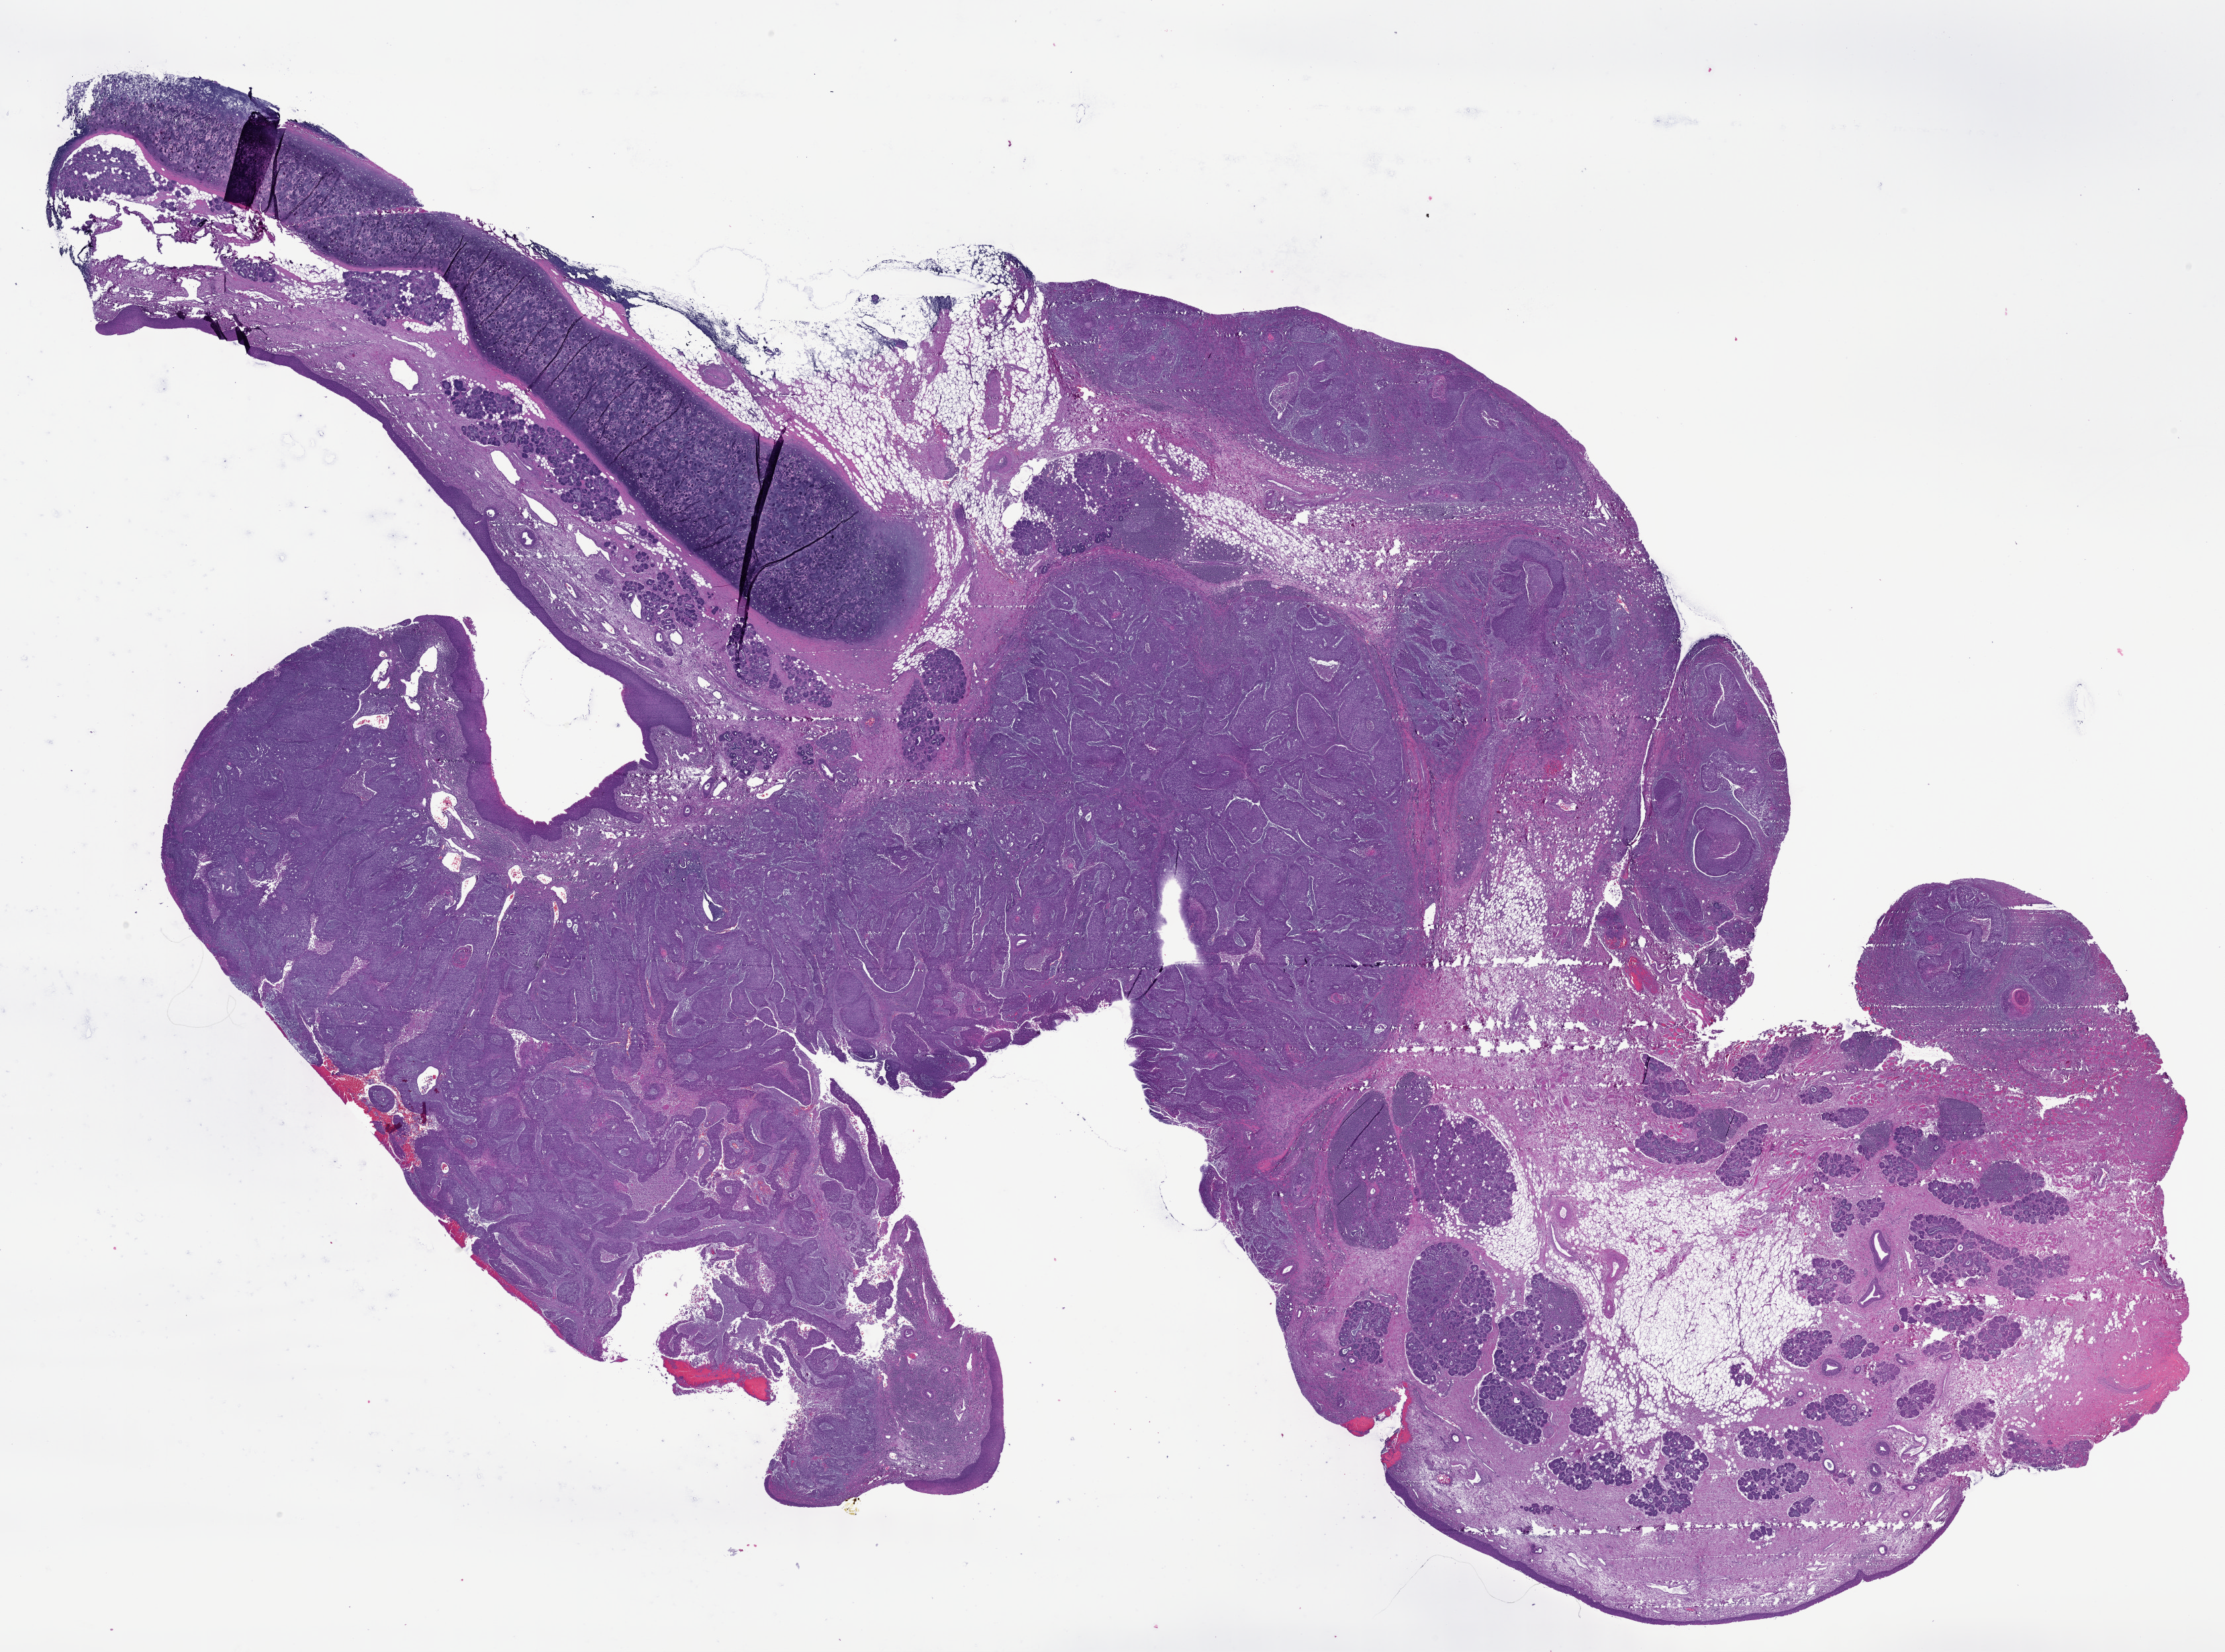
Digitized H&E-stained tissue section (whole slide), shown as a low-resolution overview of the whole scanned area (about 27.2 x 20.2 mm), formalin-fixed paraffin-embedded (FFPE) diagnostic section, primary tumour sample from the head and neck. Male patient; age at initial diagnosis 57 years. Histologic grade: G3 (poorly differentiated).
AJCC pathologic stage: IVA (7th edition). Histologic diagnosis: Squamous cell carcinoma, NOS (larynx, NOS). TNM: T4a N2b.